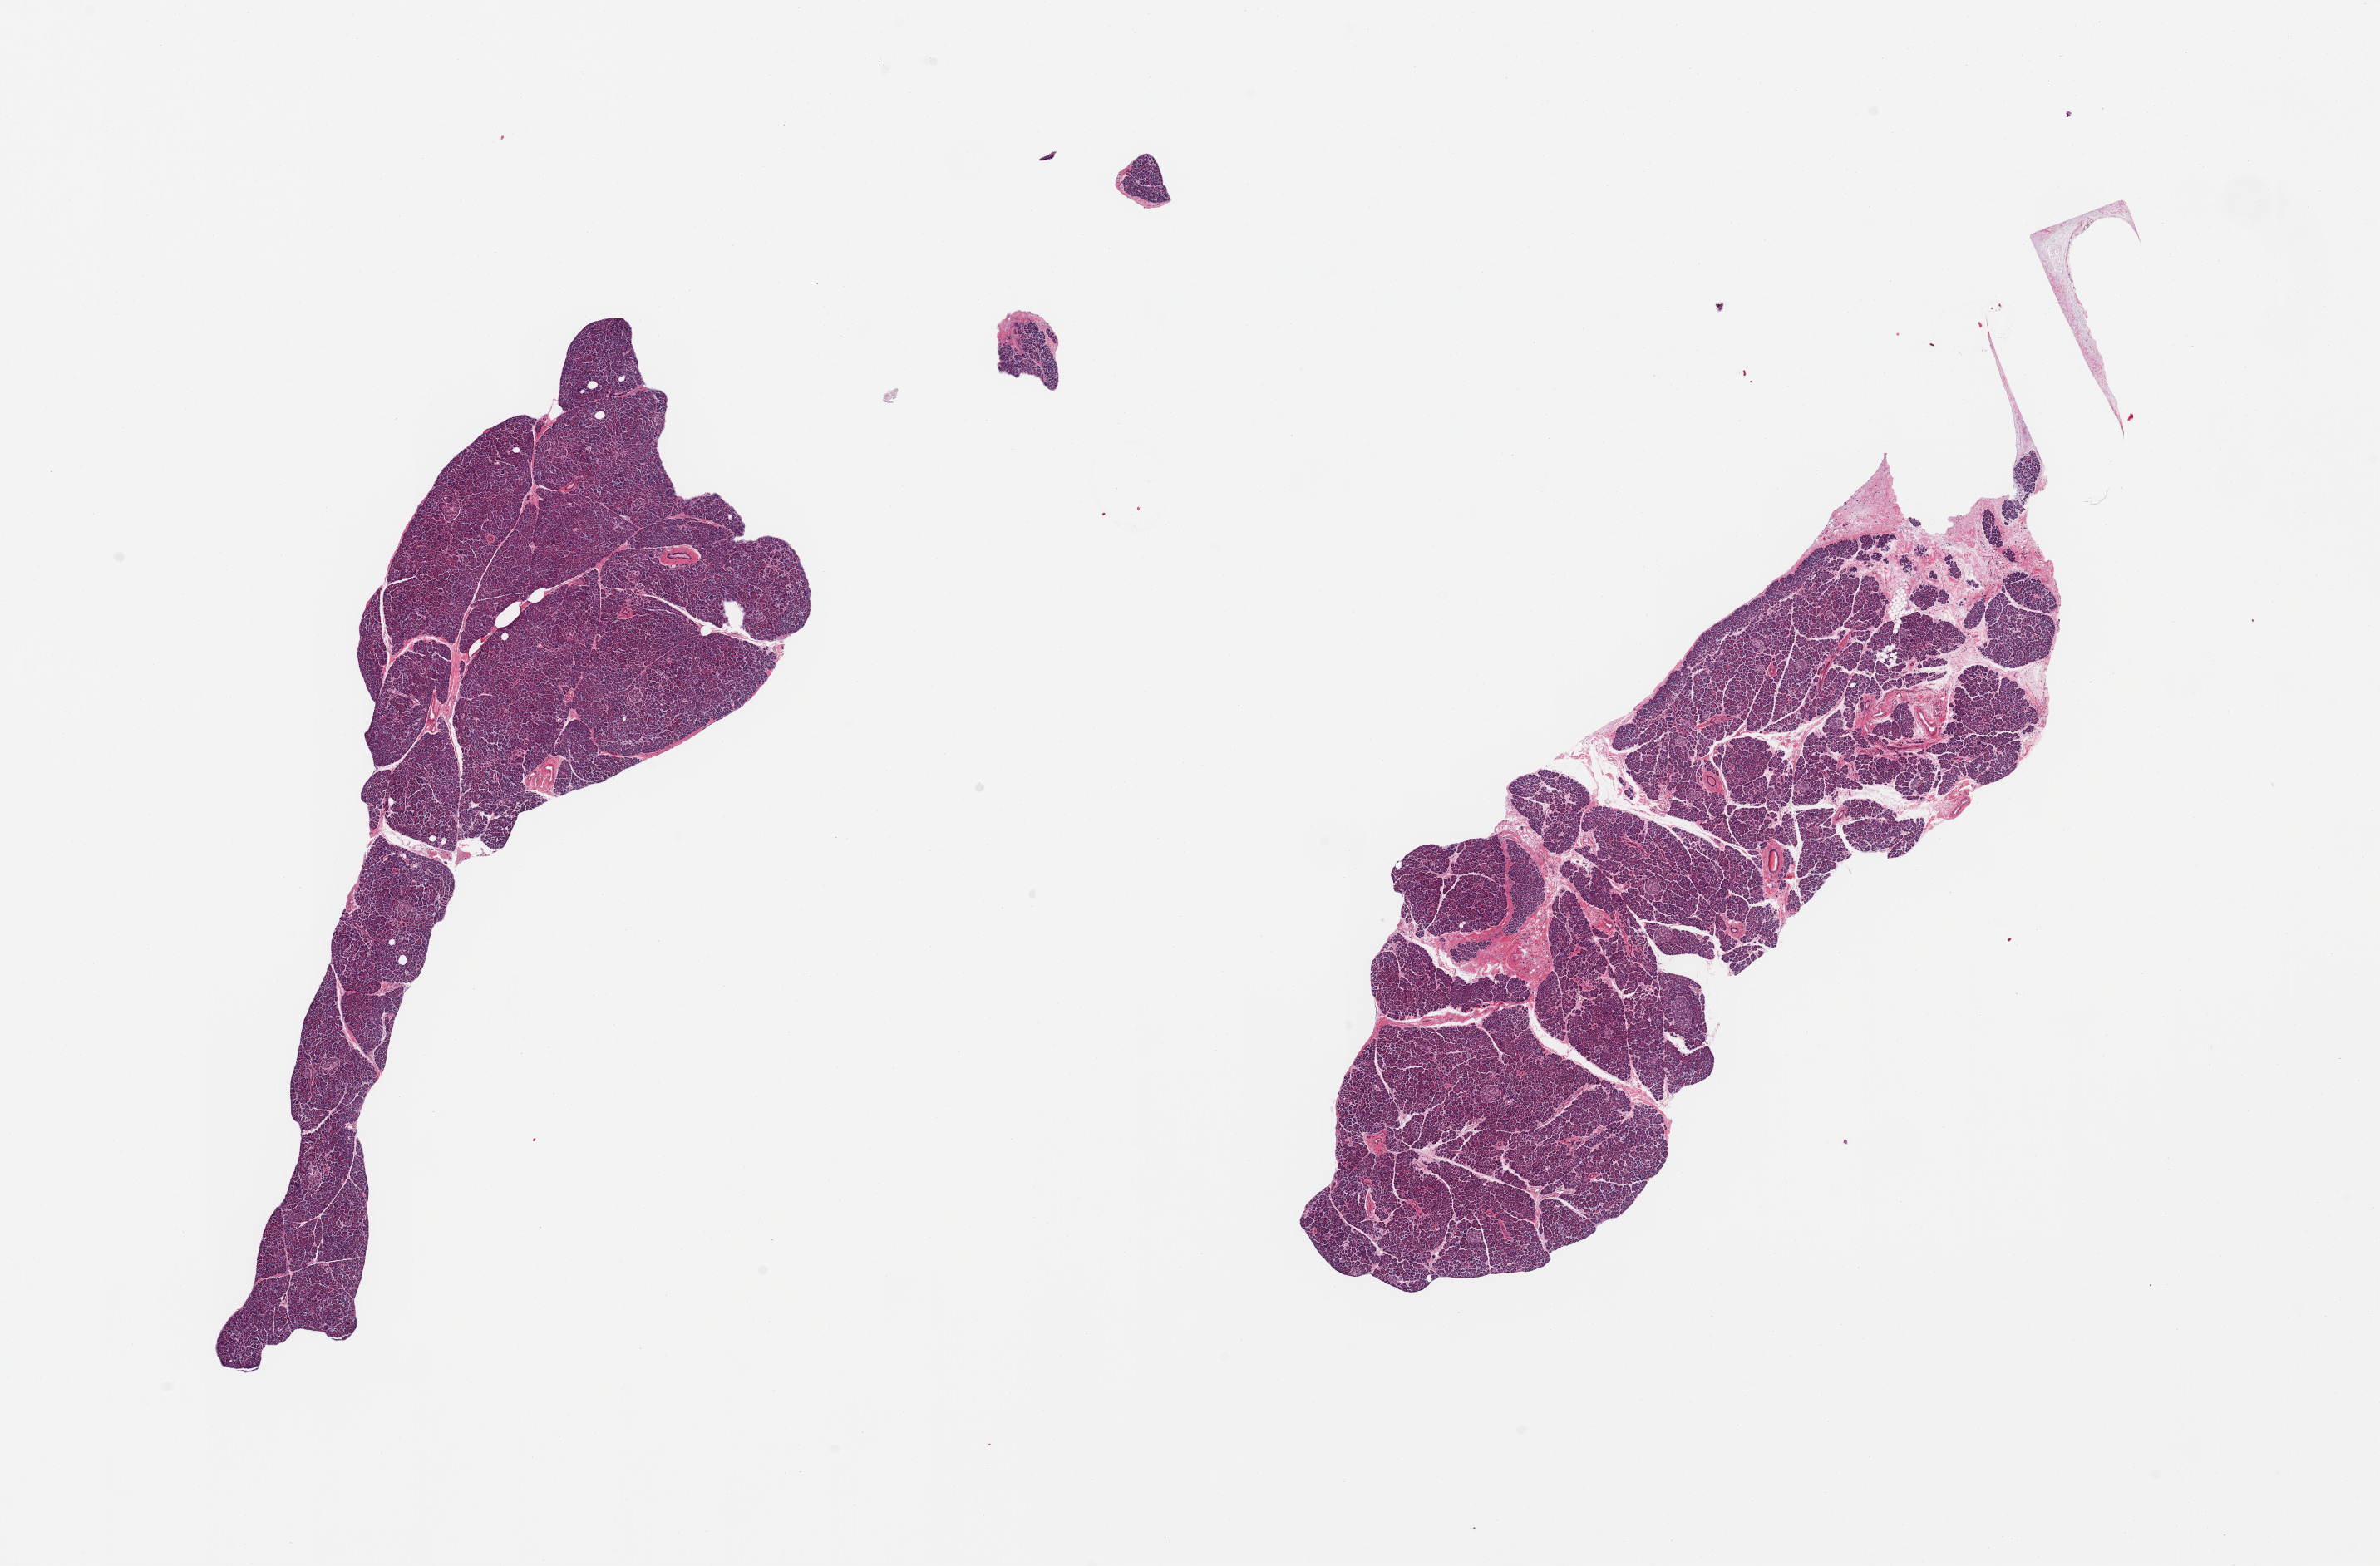
Digitized H&E-stained section, brightfield, shown as a low-resolution overview of the whole scanned area (about 22.6 x 14.9 mm, from a 20x scan). PAXgene-fixed, paraffin-embedded tissue. Sampled site (target tissue): pancreas. Tissue donor sample. Donor: female.
Review note (as recorded): 2 pieces.